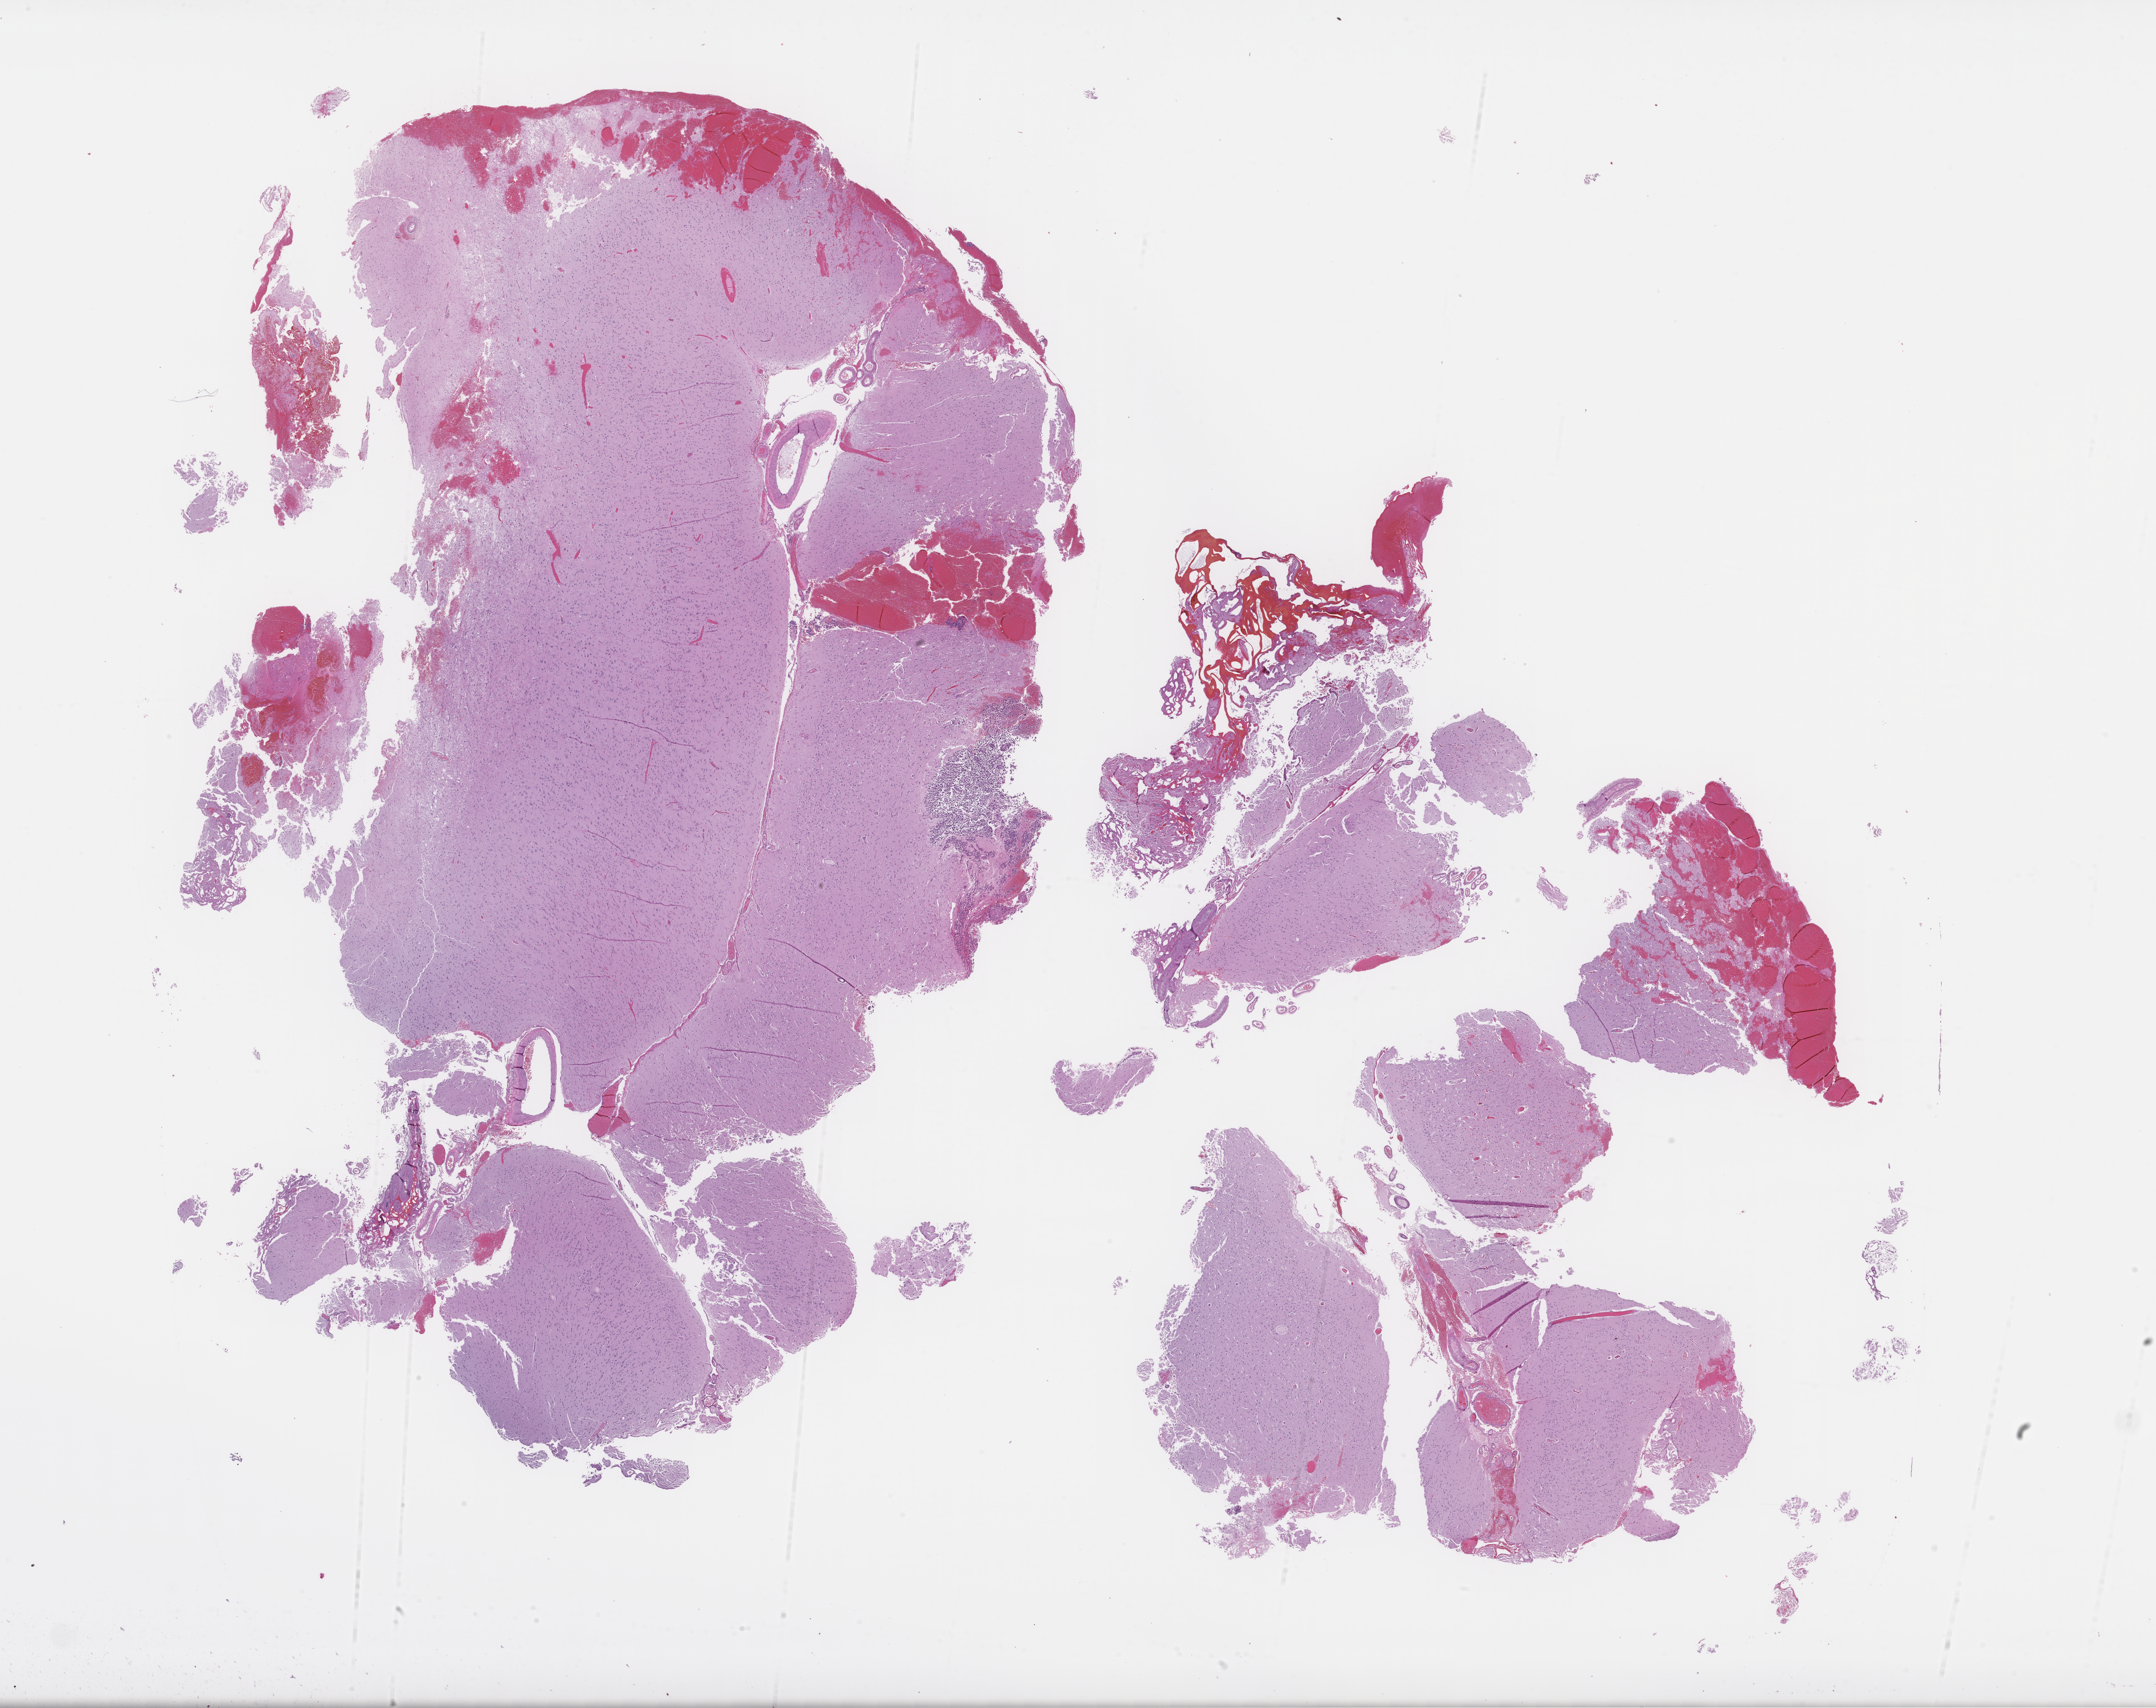
Haematoxylin and eosin whole-slide image, whole scanned area (about 29.7 x 23.5 mm) shown as a low-resolution overview. Formalin-fixed, paraffin-embedded (FFPE) tissue. Tissue site: skin. Archival tissue. Female patient.
This section: primary tumour tissue. Diagnosis: Melanoma.